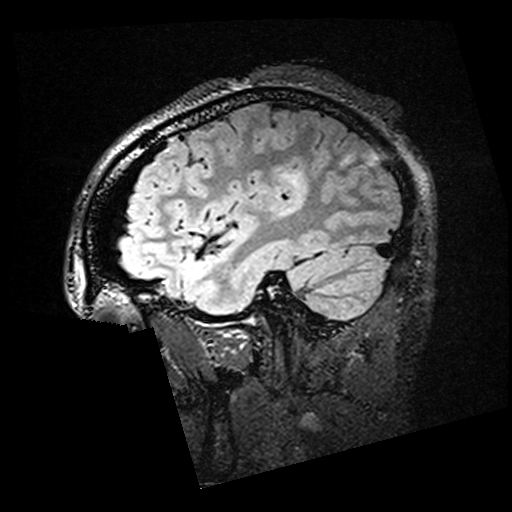
Brain MRI from a brain-tumour surgery series, one sagittal slice; position 46 of 176 along the scan axis; T2 FLAIR; 512 × 512 image matrix, field of view 250 × 250 mm. From the clinical record (not read from this slice): histopathology: Oligodendroglioma; WHO grade: 2; IDH mutation: yes.
Annotated regions visible in this slice (expert manual segmentation):
- residual tumour: box from (x=281, y=172) to (x=306, y=192) px